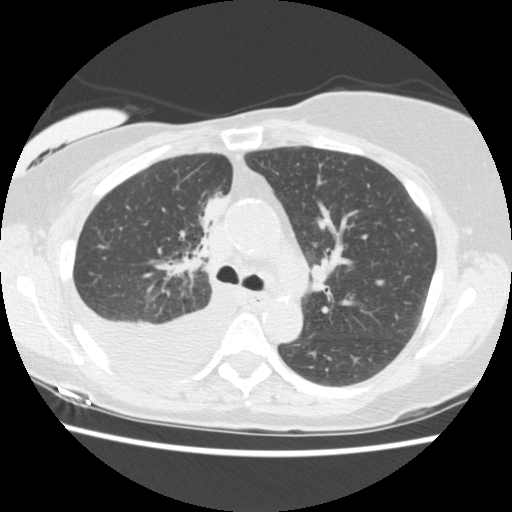
Chest CT (low-dose screening protocol), one axial image. Third screening round (two years after baseline). Lung window (W 1500 / L -600 HU). 2.5 mm slice thickness. 512 × 512 image matrix. Female participant, aged 56 years at enrolment.
Lesion marked by an expert reader, bounding box (x1, y1, x2, y2) in pixels: (181, 186, 241, 252). The screening reader recorded 2 non-calcified nodules or masses ≥4 mm on this exam (right middle lobe, right lower lobe); which of them this box marks is not recorded. Later outcome: lung cancer diagnosed 160 days after this screen — adenocarcinoma, NOS, right upper lobe, stage IIIB (AJCC 6th edition), 8 mm at pathology.